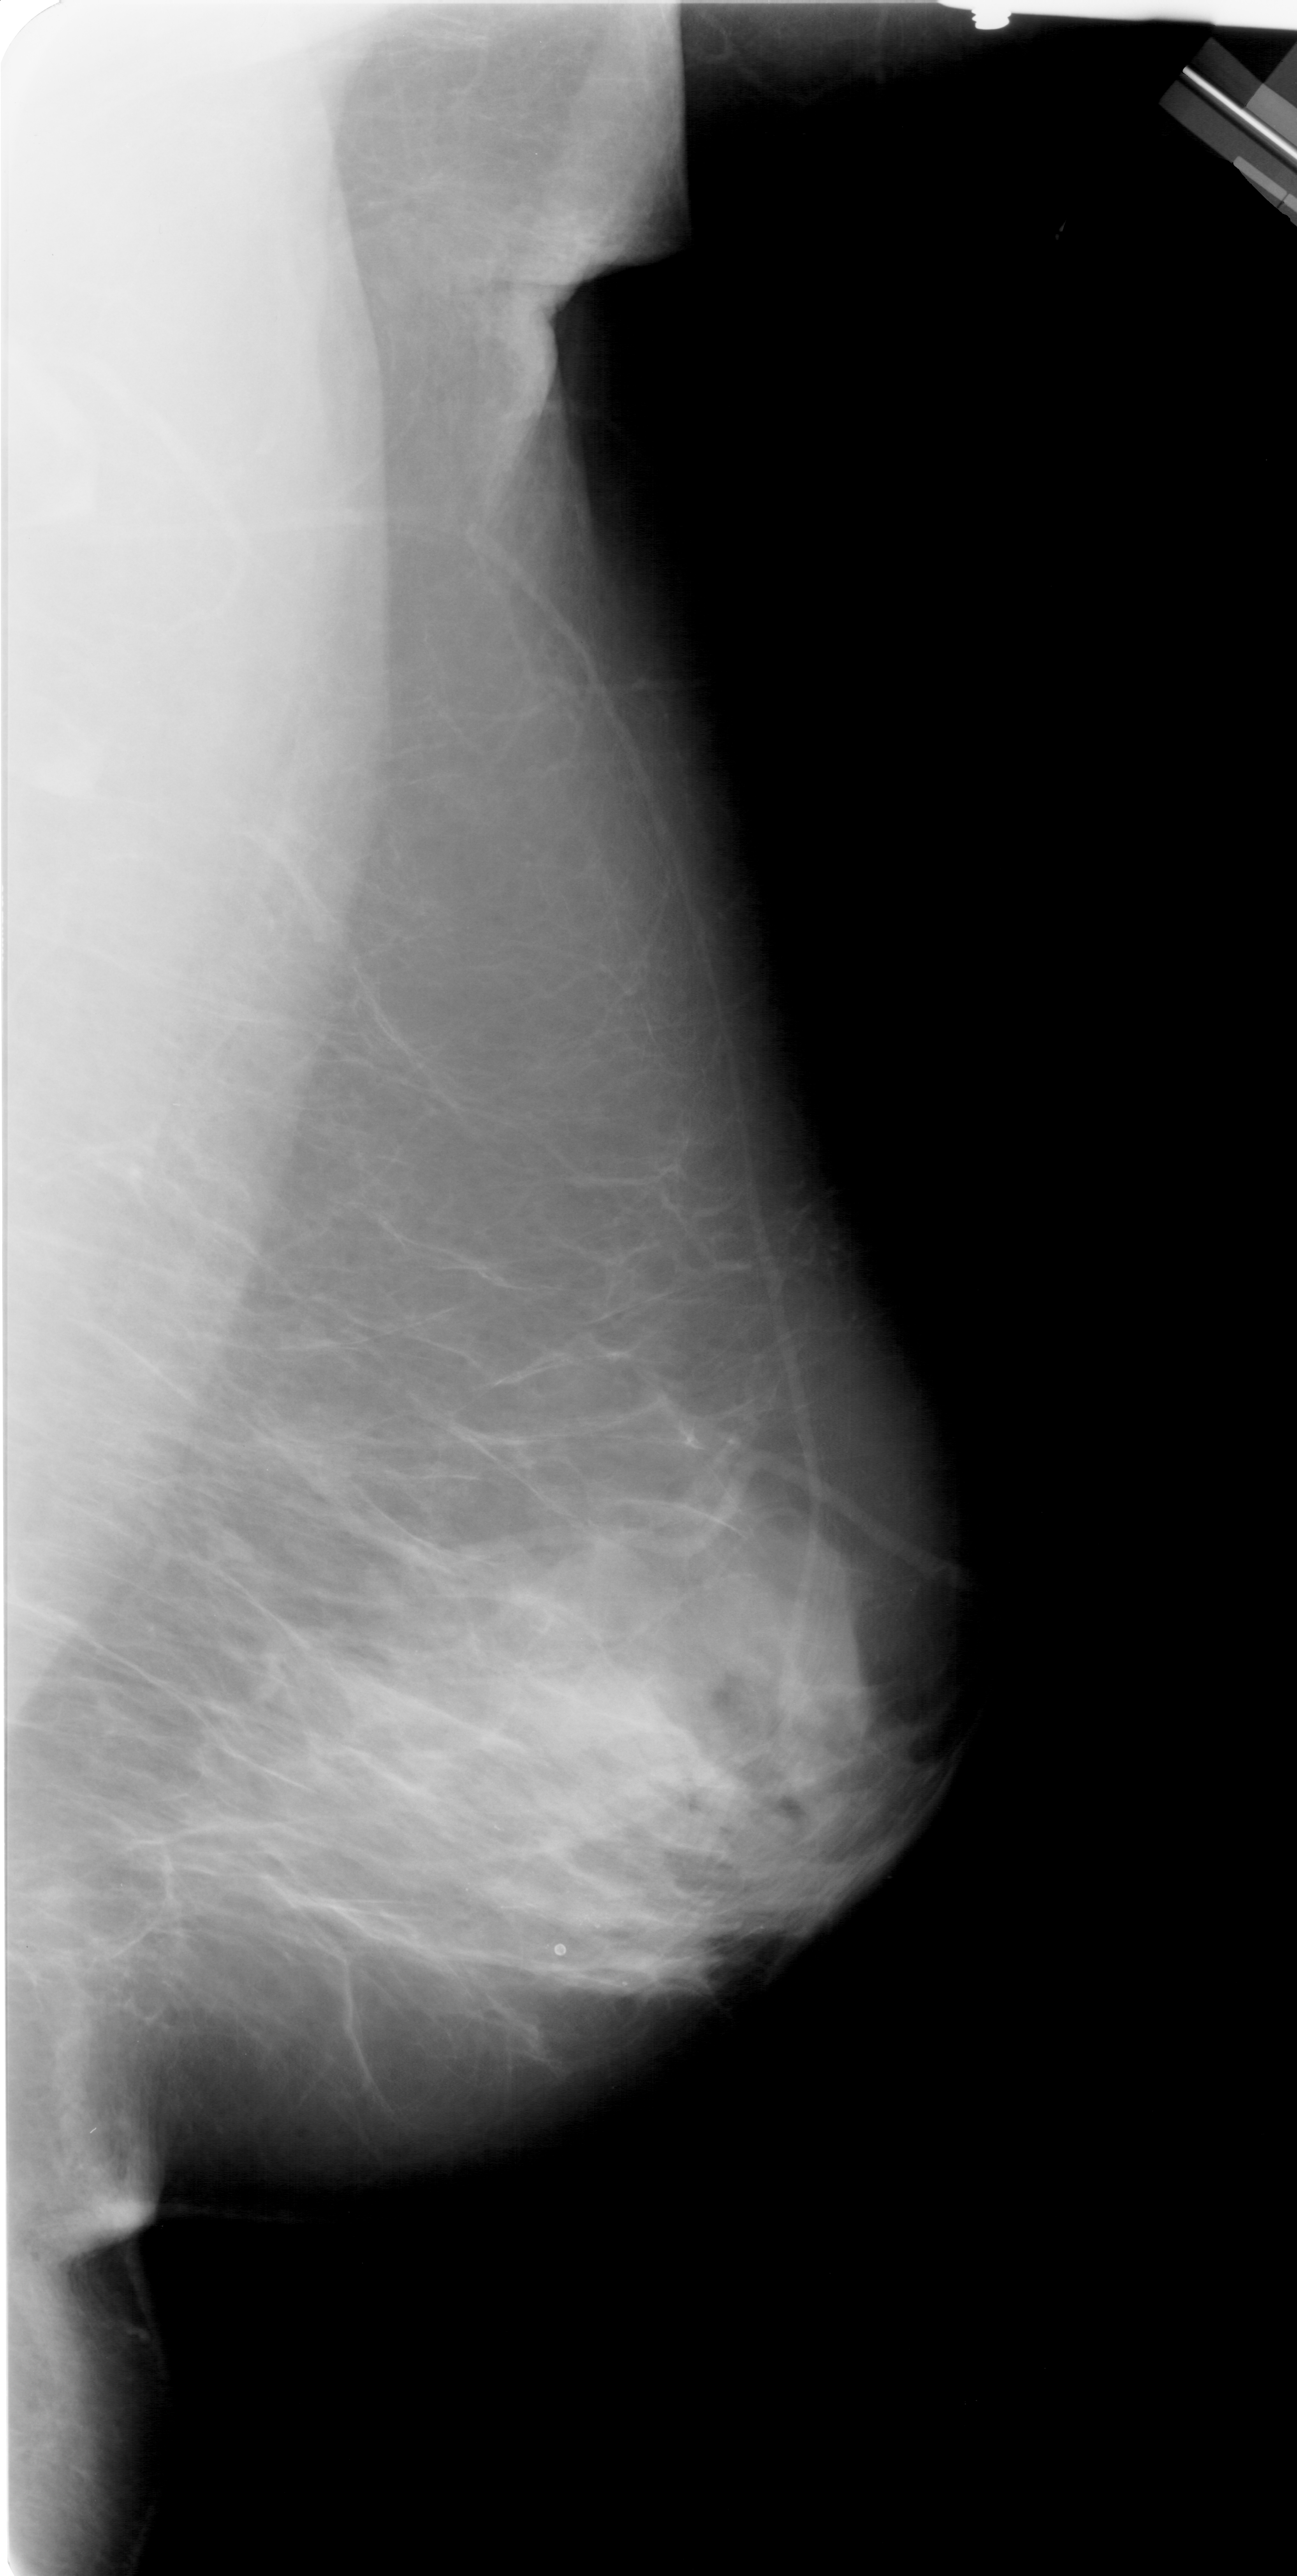
Scanned film-screen mammogram. Right breast. Mediolateral oblique (MLO) view. BI-RADS breast density category 4 (scale 1–4). 1297 × 2576 image matrix.
Expert-marked regions of interest on this film, with their recorded descriptors:
- calcifications, morphology pleomorphic, distribution linear; BI-RADS assessment category 4; subtlety rating 3 on a 1 (subtle) to 5 (obvious) scale; pathology (as recorded): benign: bounding box <381,1817,763,2024> (left, top, right, bottom; pixels)